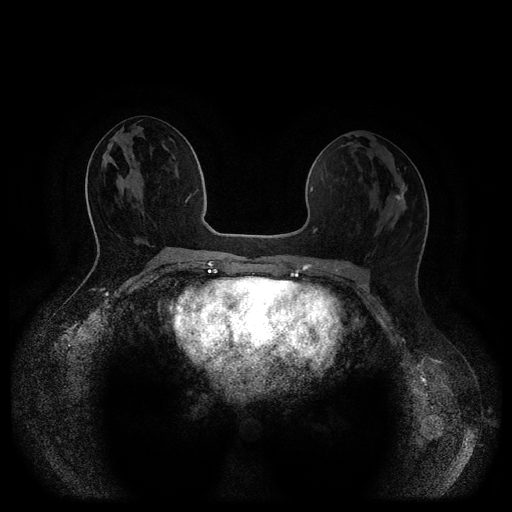
Breast MRI (dynamic contrast-enhanced, multi-phase), one axial slice; slice 49 of 116 in the series (ordered by position); dynamic contrast-enhanced series, time point 2 of 5 at this slice position (early post-contrast); 1.5 T; TE 2.6 ms, TR 5.3 ms; 2 mm slice thickness; 512 × 512 image matrix. Patient: female, 27 years.
Outlined on this slice (semi-automatically segmented with operator editing):
- breast lesion (labelled 'tumour' in the annotation; benign lesions carry a separate 'benign' label): bounding box <395,183,407,202> (left, top, right, bottom; pixels)